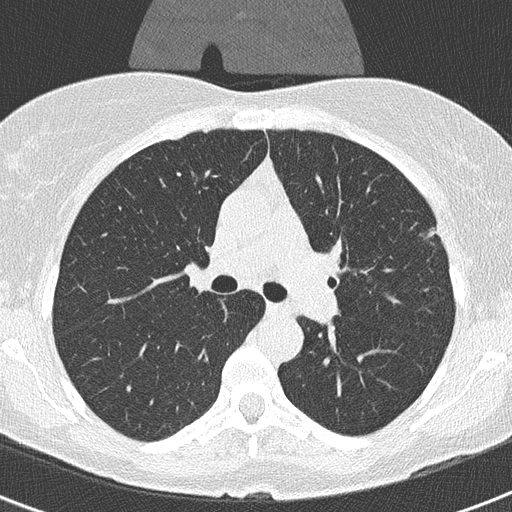
Low-dose screening chest CT, one axial slice; slice 213 of 320 in the series (ordered by position); 120 kVp; lung window (W 1500 / L -600 HU); 2 mm slice thickness; 512 × 512 image matrix.
Structures marked on this image (outlined manually by an expert reader):
- lesion 1 (tumor, upper lobe of left lung): box from (x=426, y=230) to (x=435, y=238) px